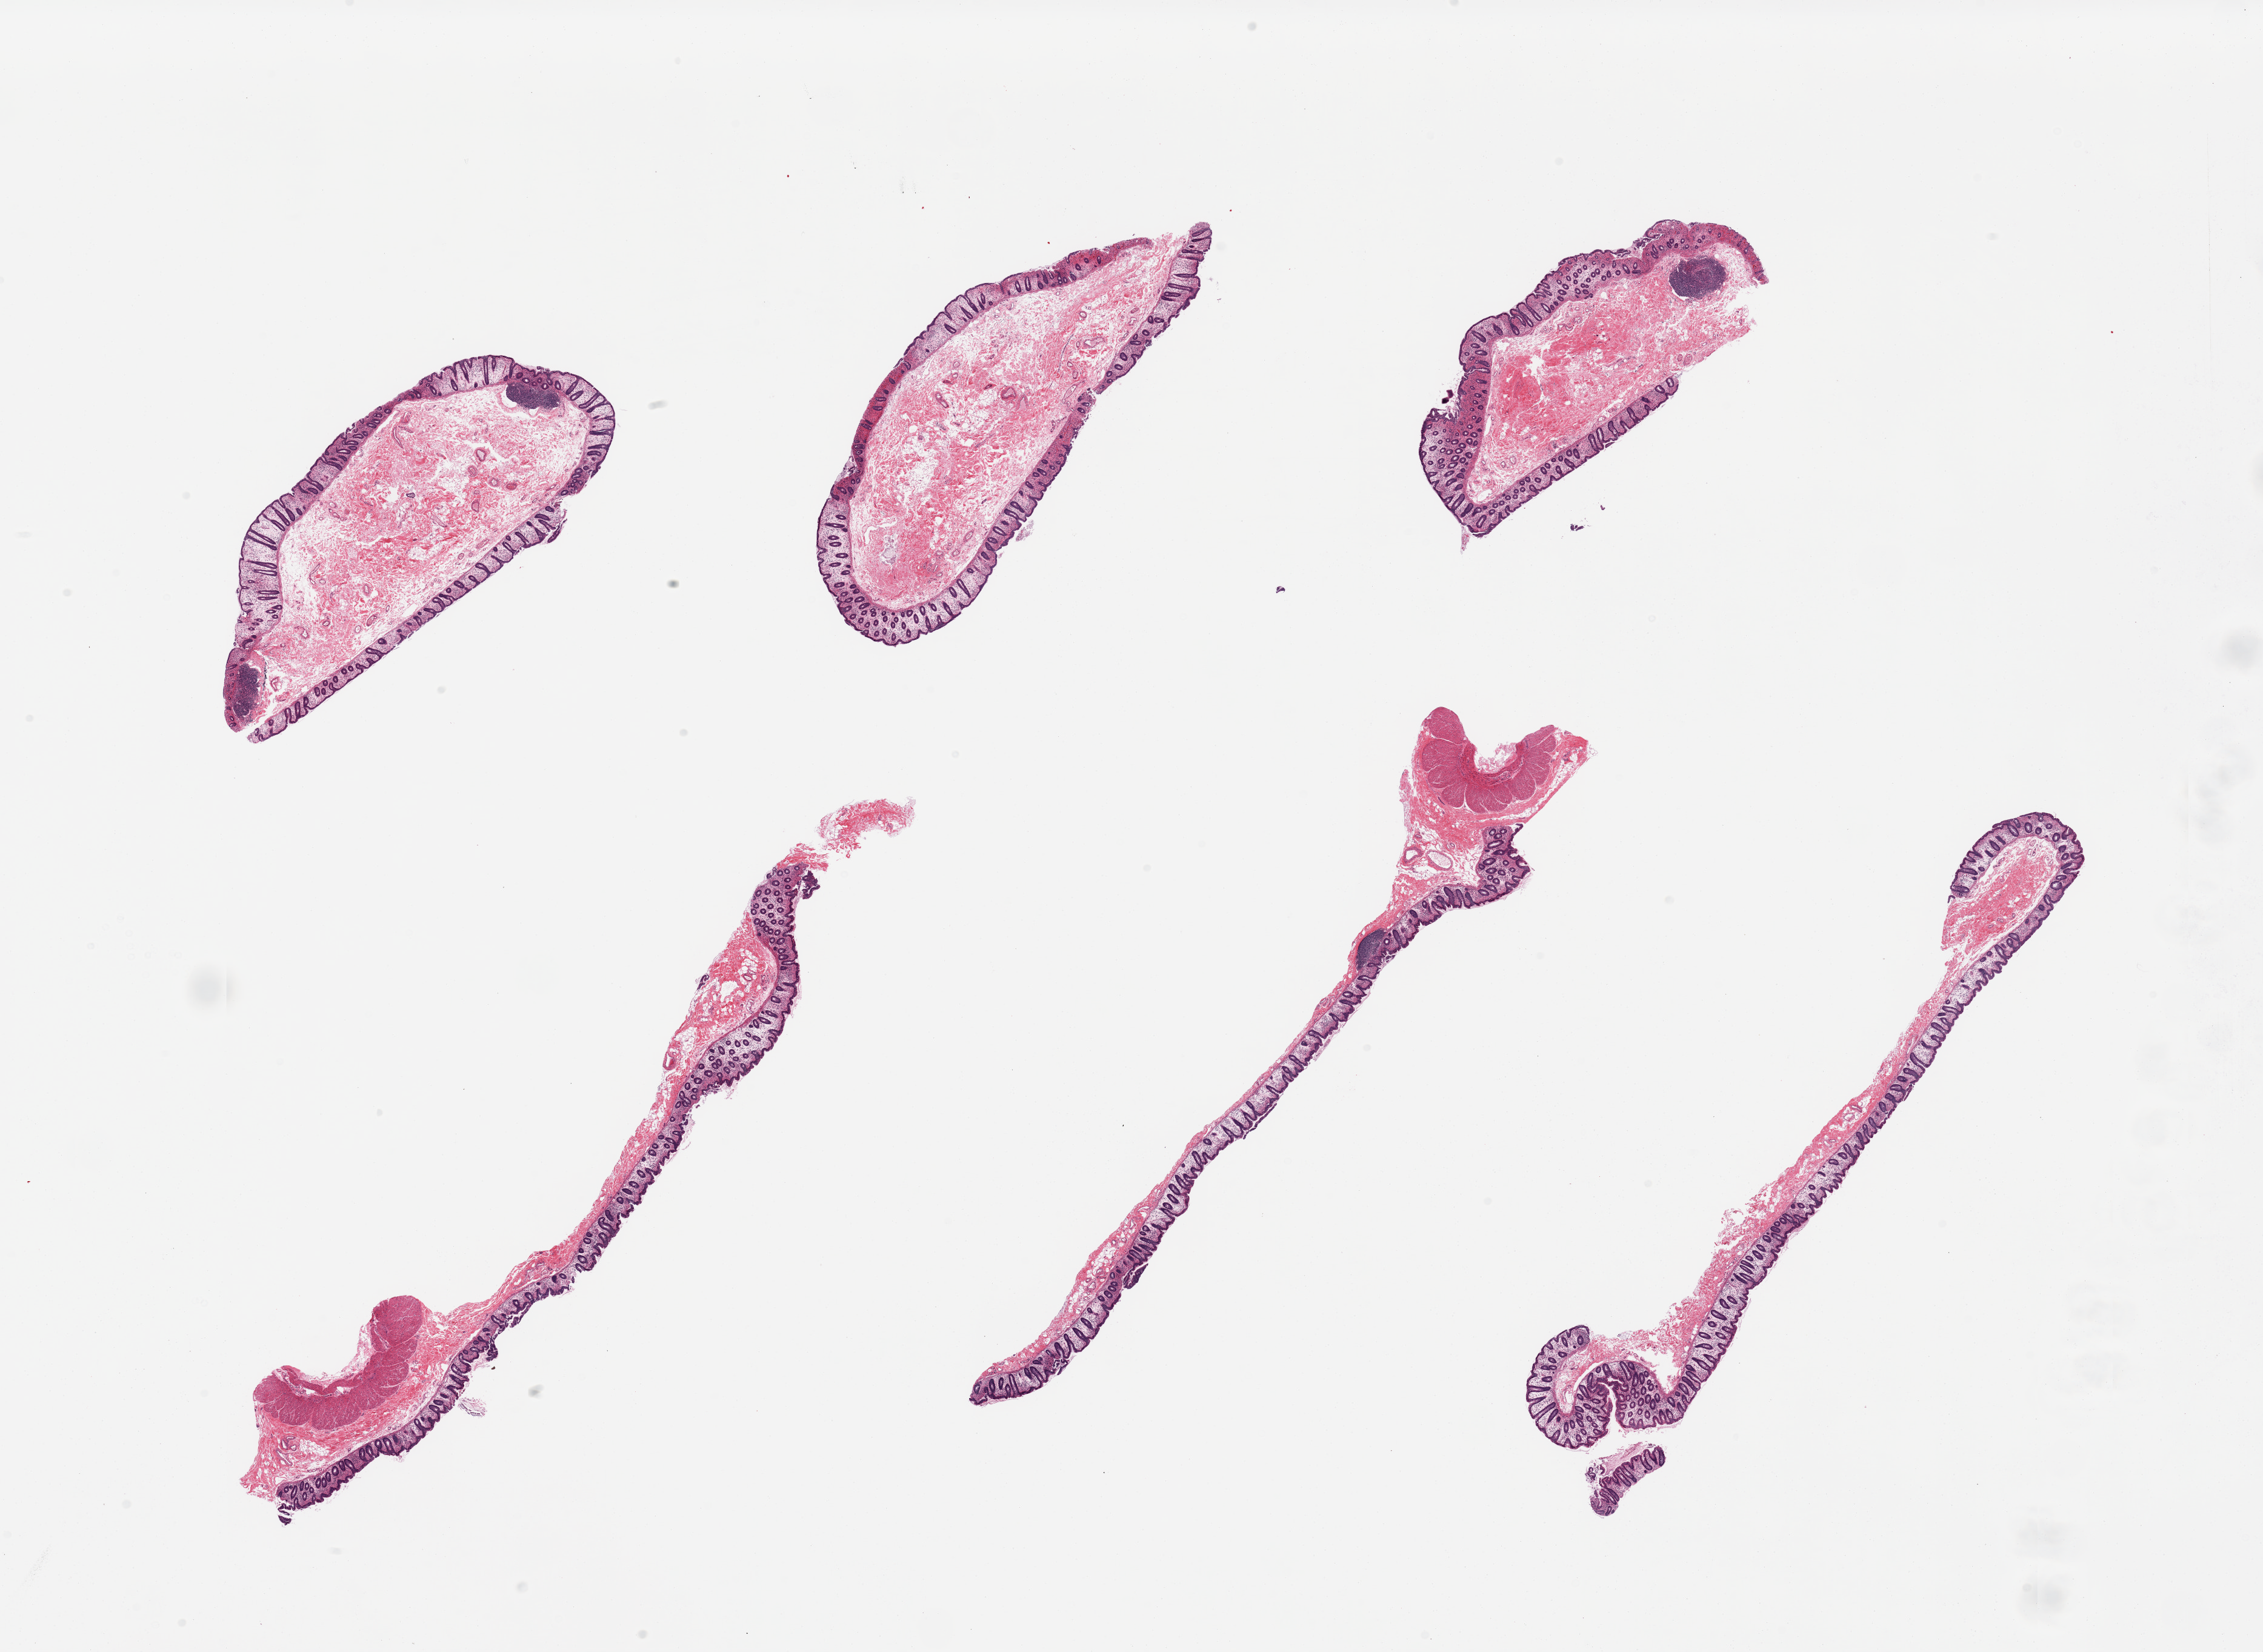
Digitized H&E-stained section, low-resolution overview of the scanned area, about 29.5 x 21.6 mm (slide scanned at 20x), PAXgene-fixed, paraffin-embedded tissue, target tissue: transverse colon, tissue donor sample. Male donor.
* pathologist's review note for this sample: 6 pieces, predominantly mucosa with few strips of muscularis, edema and ischemic change